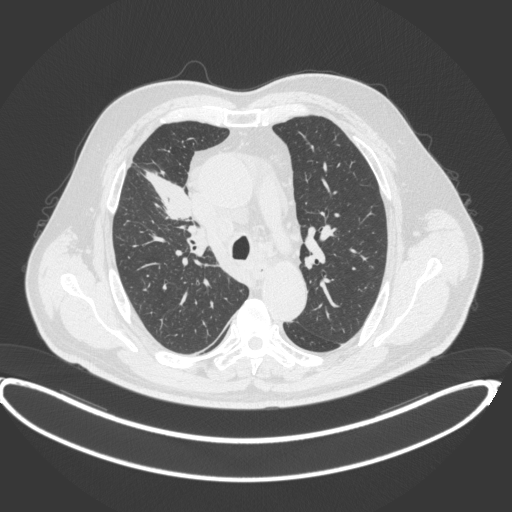
Chest CT, one axial slice. Reconstruction kernel B31f. 120 kVp. Lung window (W 1500 / L -600 HU). 1 mm slice thickness. 512 × 512 image matrix, field of view 448 × 448 mm. Male patient, age 62 years. From the clinical record (not read from this slice): clinical TNM (as recorded): T1c N3 M1c.
Annotated regions visible in this slice (bounding box drawn by a radiologist):
- lung tumour (recorded histology: adenocarcinoma): bounding box <138,166,192,221> (left, top, right, bottom; pixels)